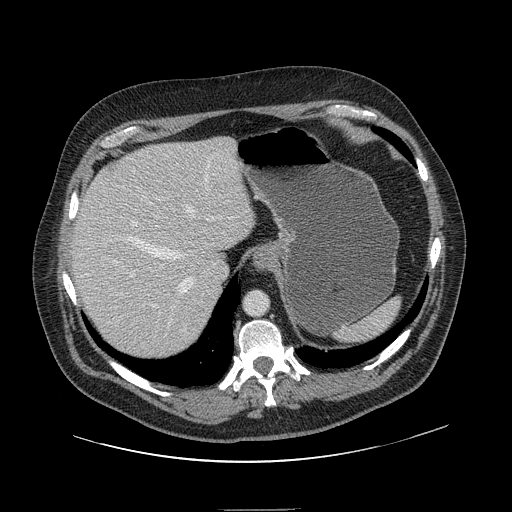
Contrast-enhanced abdominal CT, one axial slice. Position 115 of 154 along the scan axis. 120 kVp. Intravenous contrast given. Soft-tissue window (W 400 / L 40 HU). 2.5 mm slice thickness. 512 × 512 image matrix, field of view 451 × 451 mm. Male patient, age 61 years. From the clinical record (not read from this slice): diagnosis: colorectal cancer liver metastases, imaged before liver resection; multiple liver metastases: yes; largest metastasis: 2.6 cm.
Structures marked on this image (expert manual segmentation):
- hepatic veins: bounding box <128,195,220,294> (left, top, right, bottom; pixels)
- liver: <71,138,256,361>
- planned liver remnant (the part of the liver to remain after resection): <71,143,255,355>
- portal vein (with intrahepatic branches): <130,197,221,307>